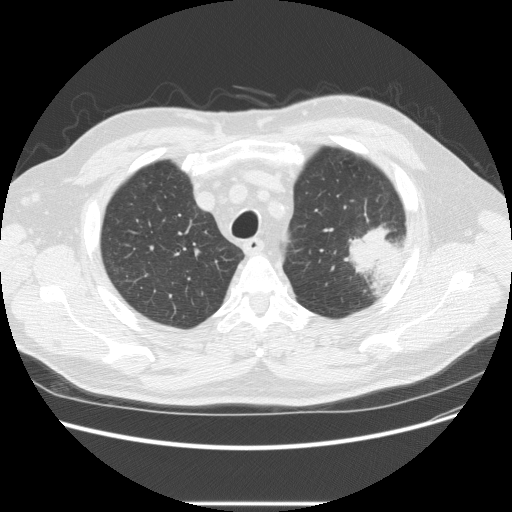
Low-dose screening chest CT, one axial slice; position 184 of 233 along the scan axis; 120 kVp; lung window (W 1500 / L -600 HU); 2.5 mm slice thickness; 512 × 512 image matrix, field of view 380 × 380 mm.
Annotated regions visible in this slice (expert manual segmentation):
- lesion 1 (tumor, upper lobe of left lung): bounding box [x1, y1, x2, y2] px = [343, 223, 402, 297]